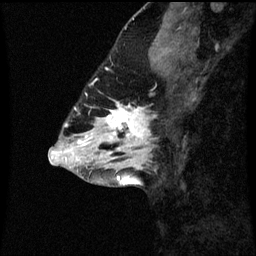
Breast MRI (dynamic contrast-enhanced), one sagittal slice. Position 27 of 60 along the scan axis. Dynamic contrast-enhanced series, image 2 of 3 at this slice position (ordered by acquisition). 1.5 T. TE 4.2 ms, TR 8.9 ms. 256 × 256 image matrix, field of view 200 × 200 mm. Female patient, age 43 years. From the clinical record (not read from this slice): setting: breast cancer imaged before/during neoadjuvant chemotherapy; receptor status: HR-positive, HER2-negative.
Structures marked on this image (semi-automatic segmentation, software-assisted and operator-edited):
- analysis volume of interest (the breast-tissue region the enhancement analysis was run in; not a lesion): bounding box (x1, y1, x2, y2) in pixels: (96, 102, 157, 159)
- tumour enhancement mask (voxels above the 70 % enhancement threshold inside the analysis volume of interest): (106, 104, 151, 153)